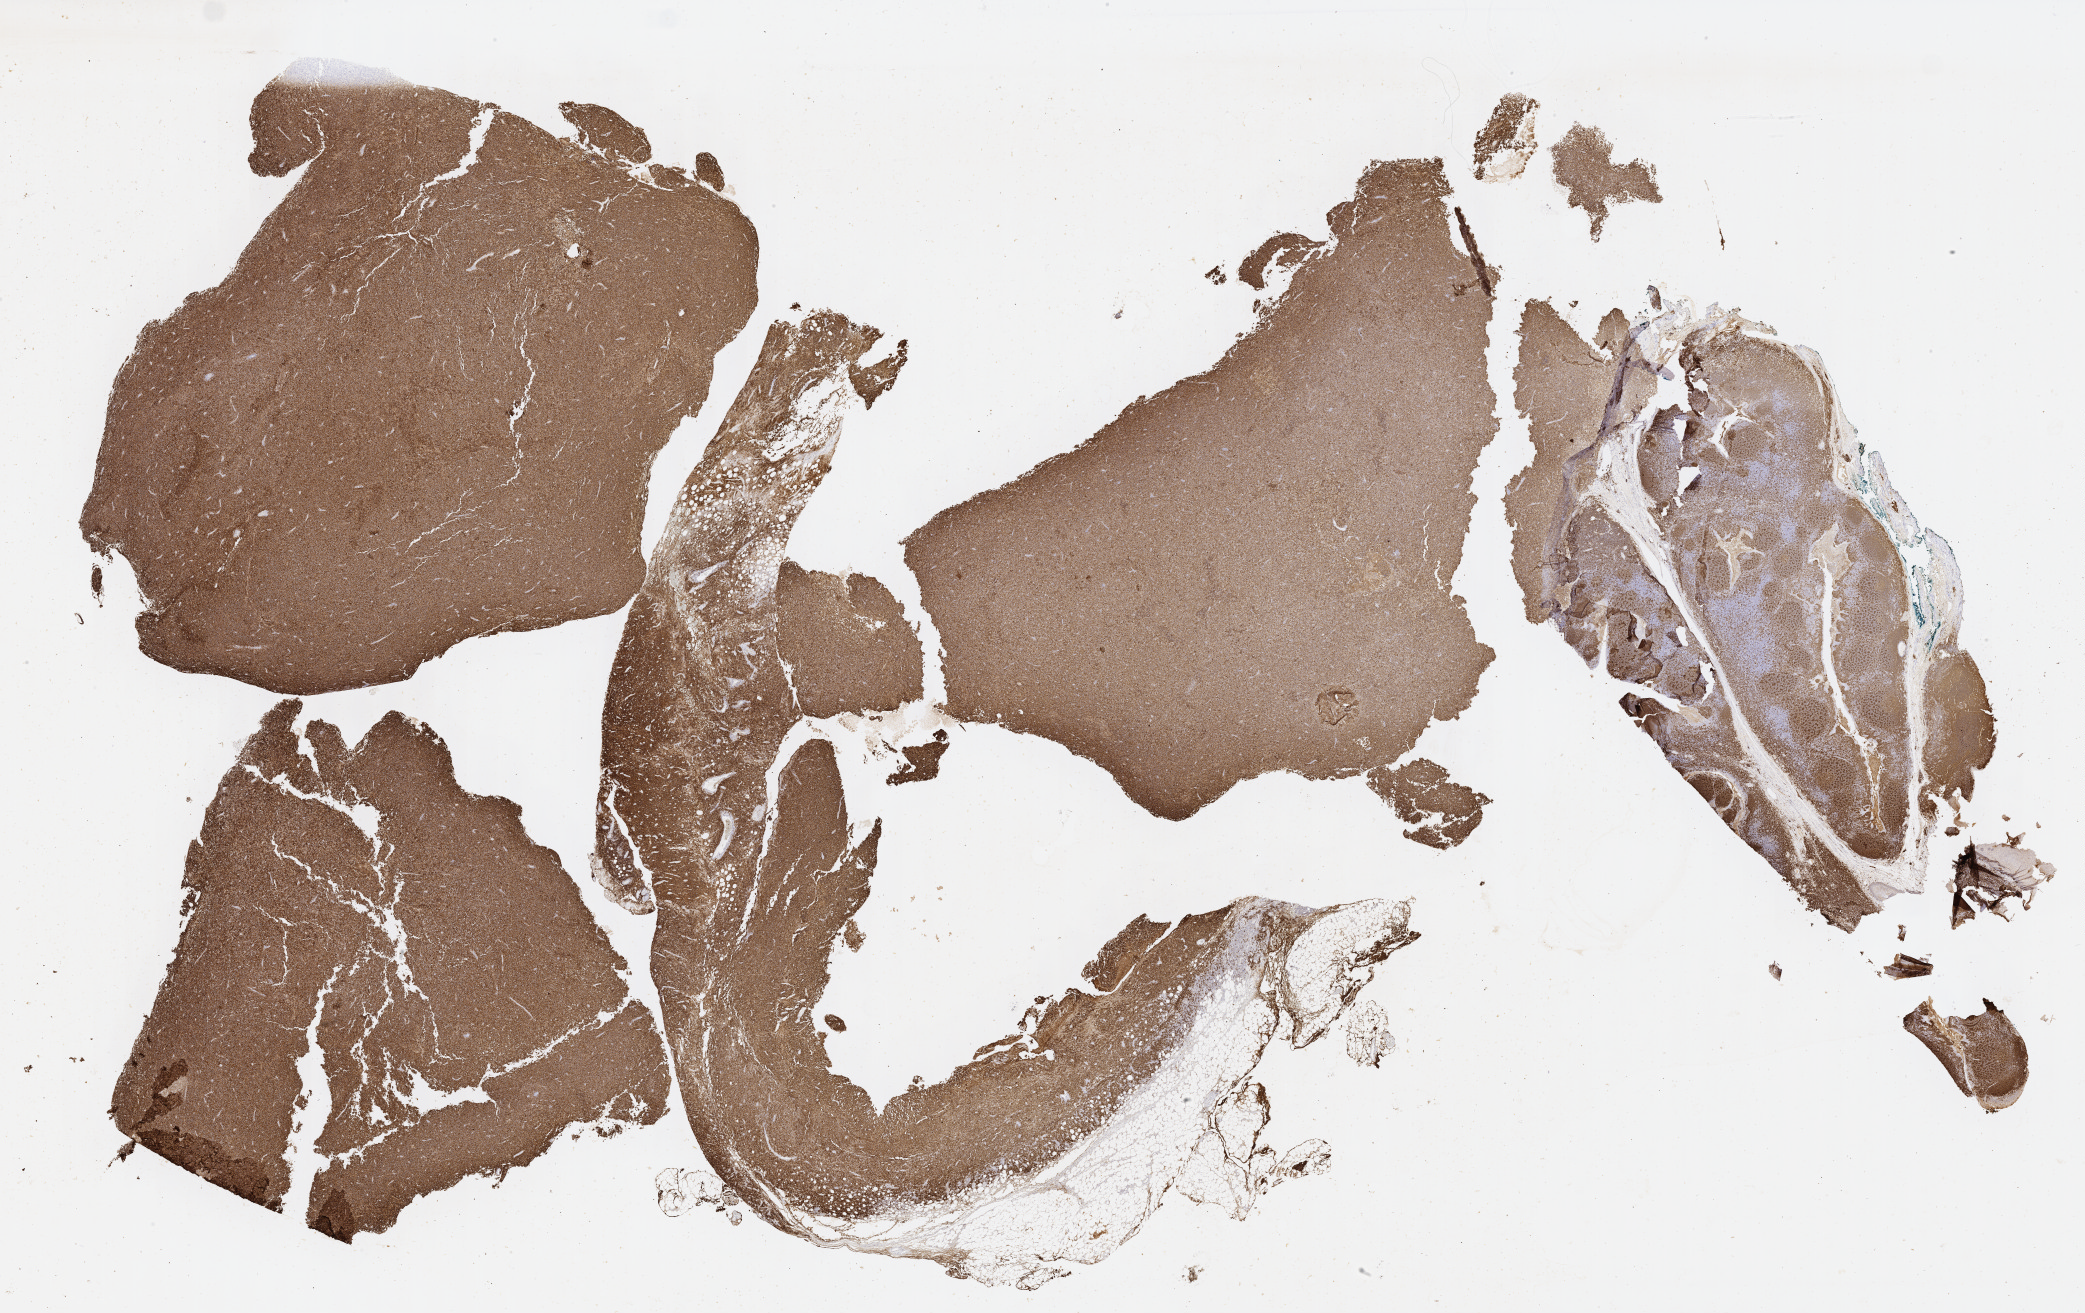
Immunohistochemistry (IHC) whole-slide image stained for CD20, shown as a low-resolution overview of the whole scanned area (about 33.7 x 21.2 mm). Patient sex: female.
Specimen: tumor tissue.